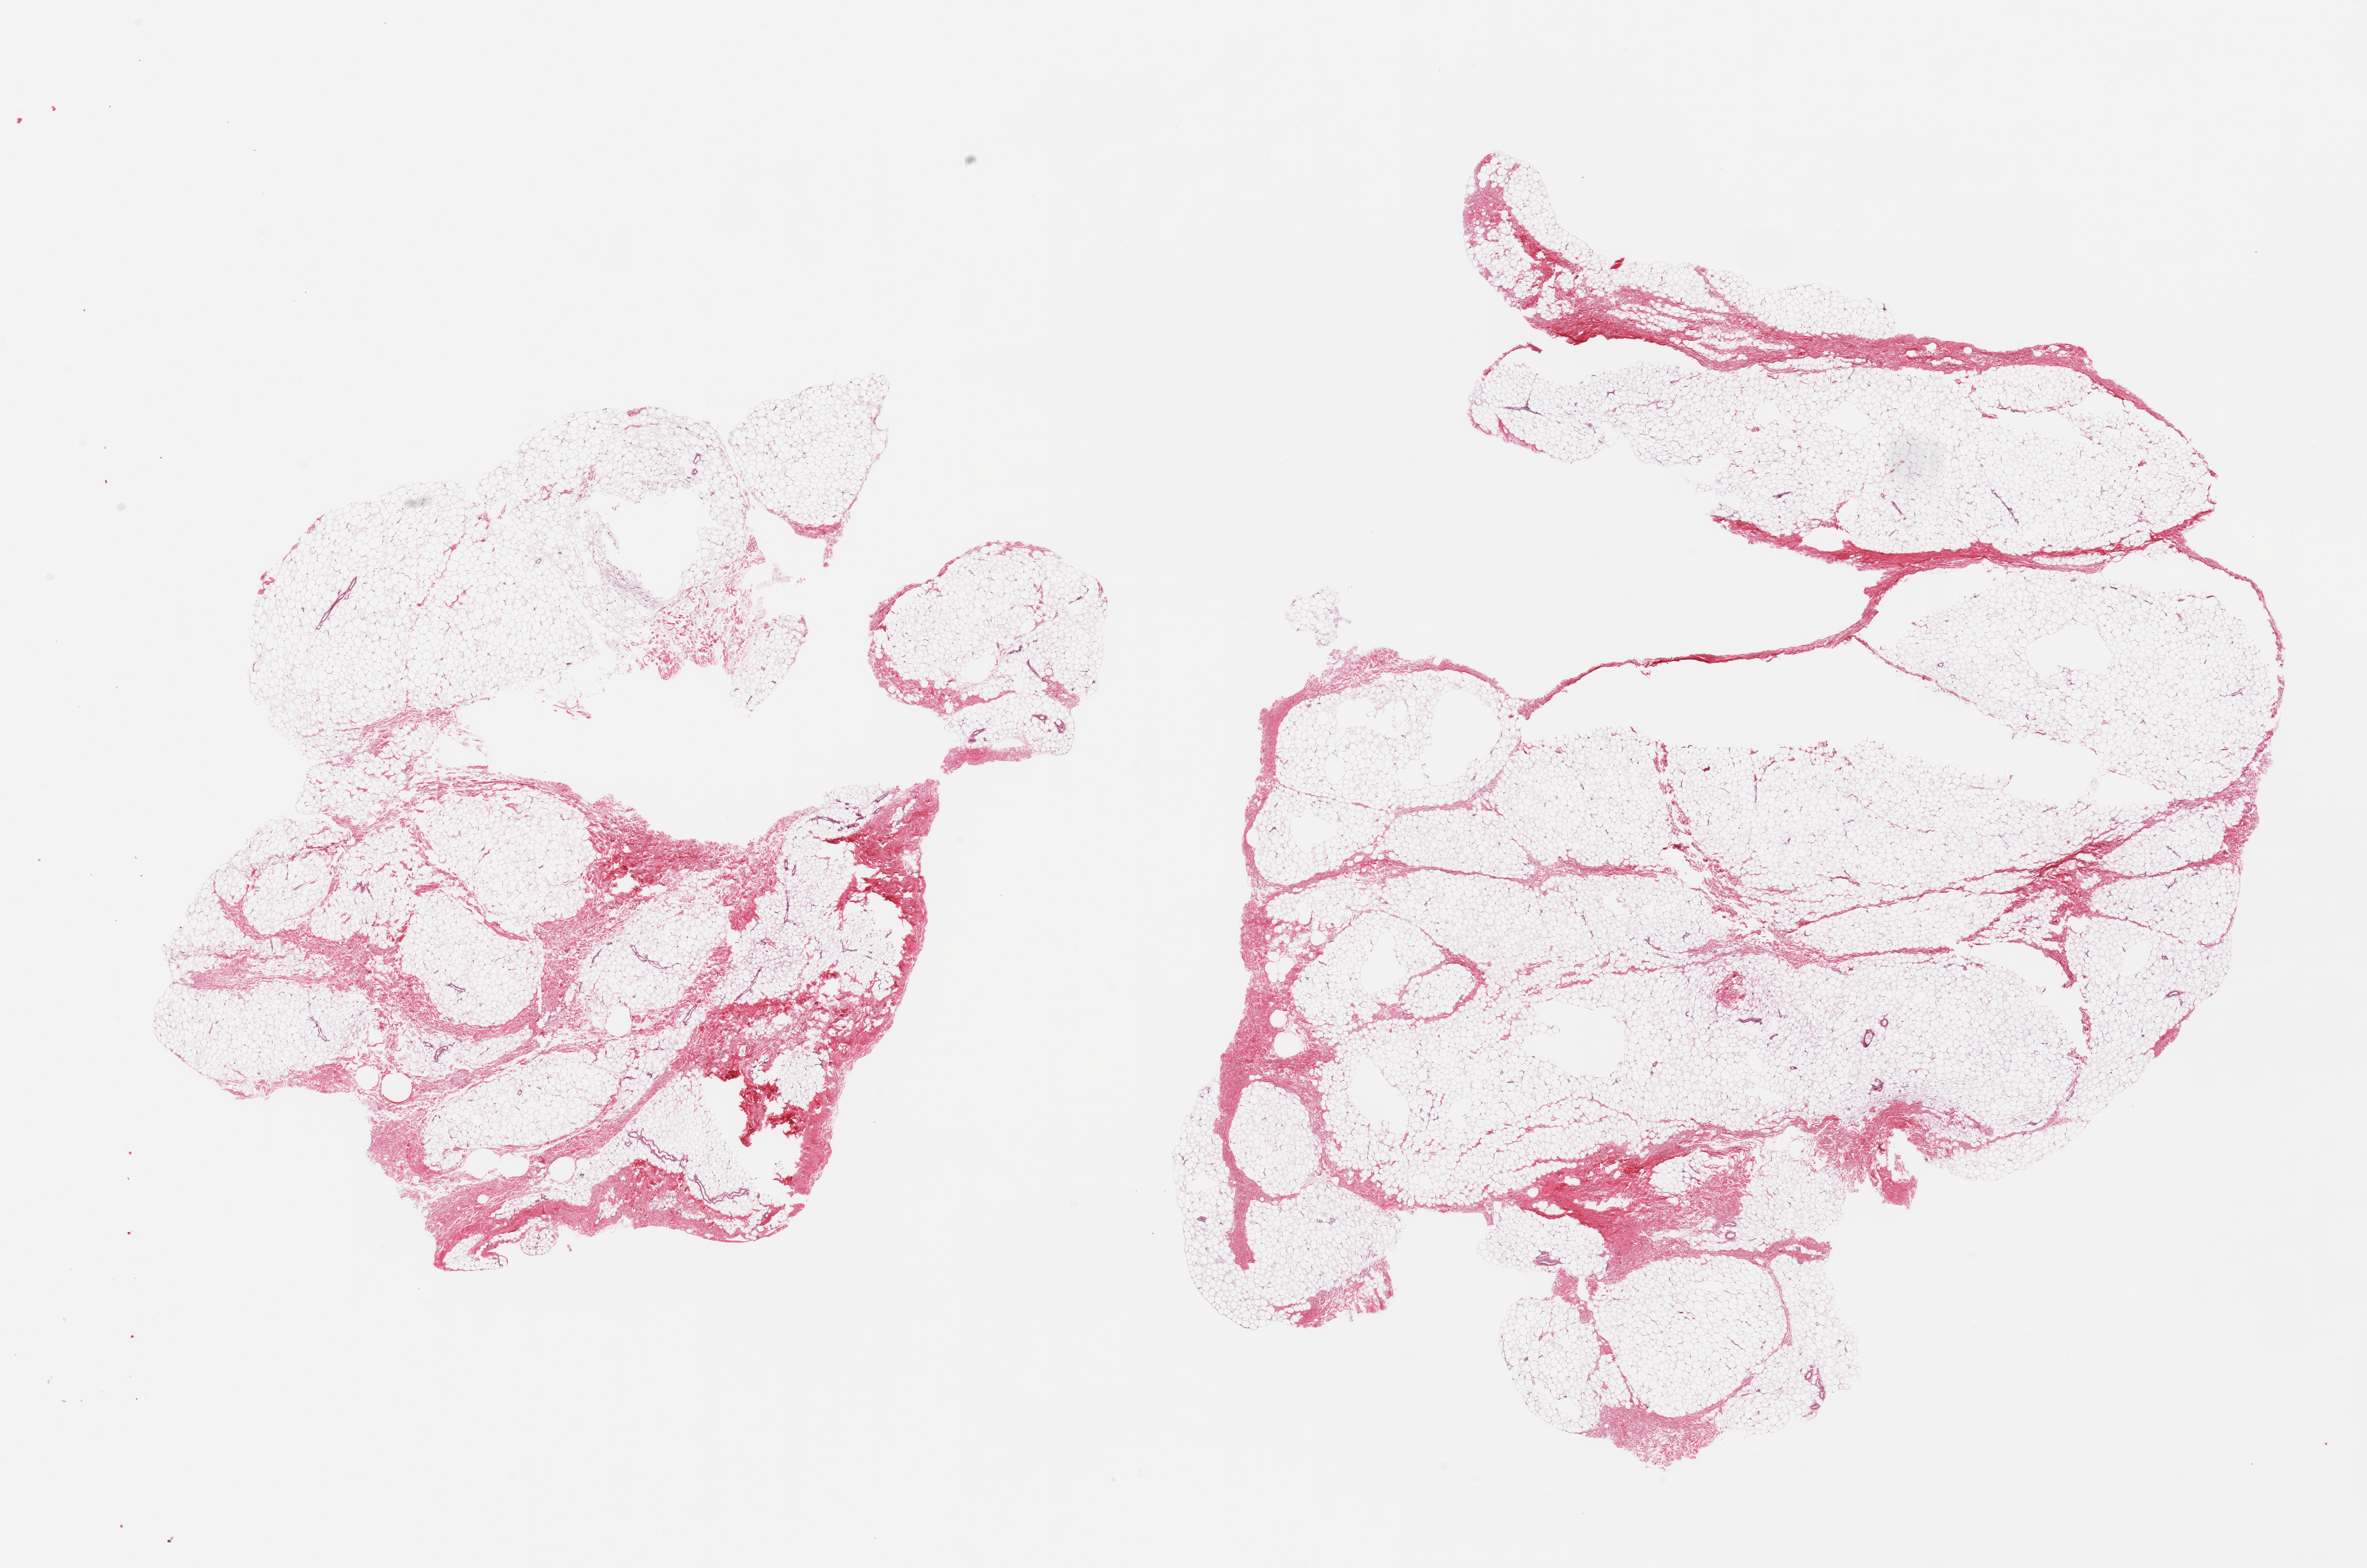
Whole-slide image, H&E stain, low-resolution overview of the scanned area, about 26.6 x 17.6 mm (slide scanned at 20x). PAXgene-fixed, paraffin-embedded tissue. Section of breast (target tissue). Tissue donor sample. Male donor.
Pathologist's review note for this sample: 2 pieces; fat admixed with fibrocollagenous tissue, no ductal elements.